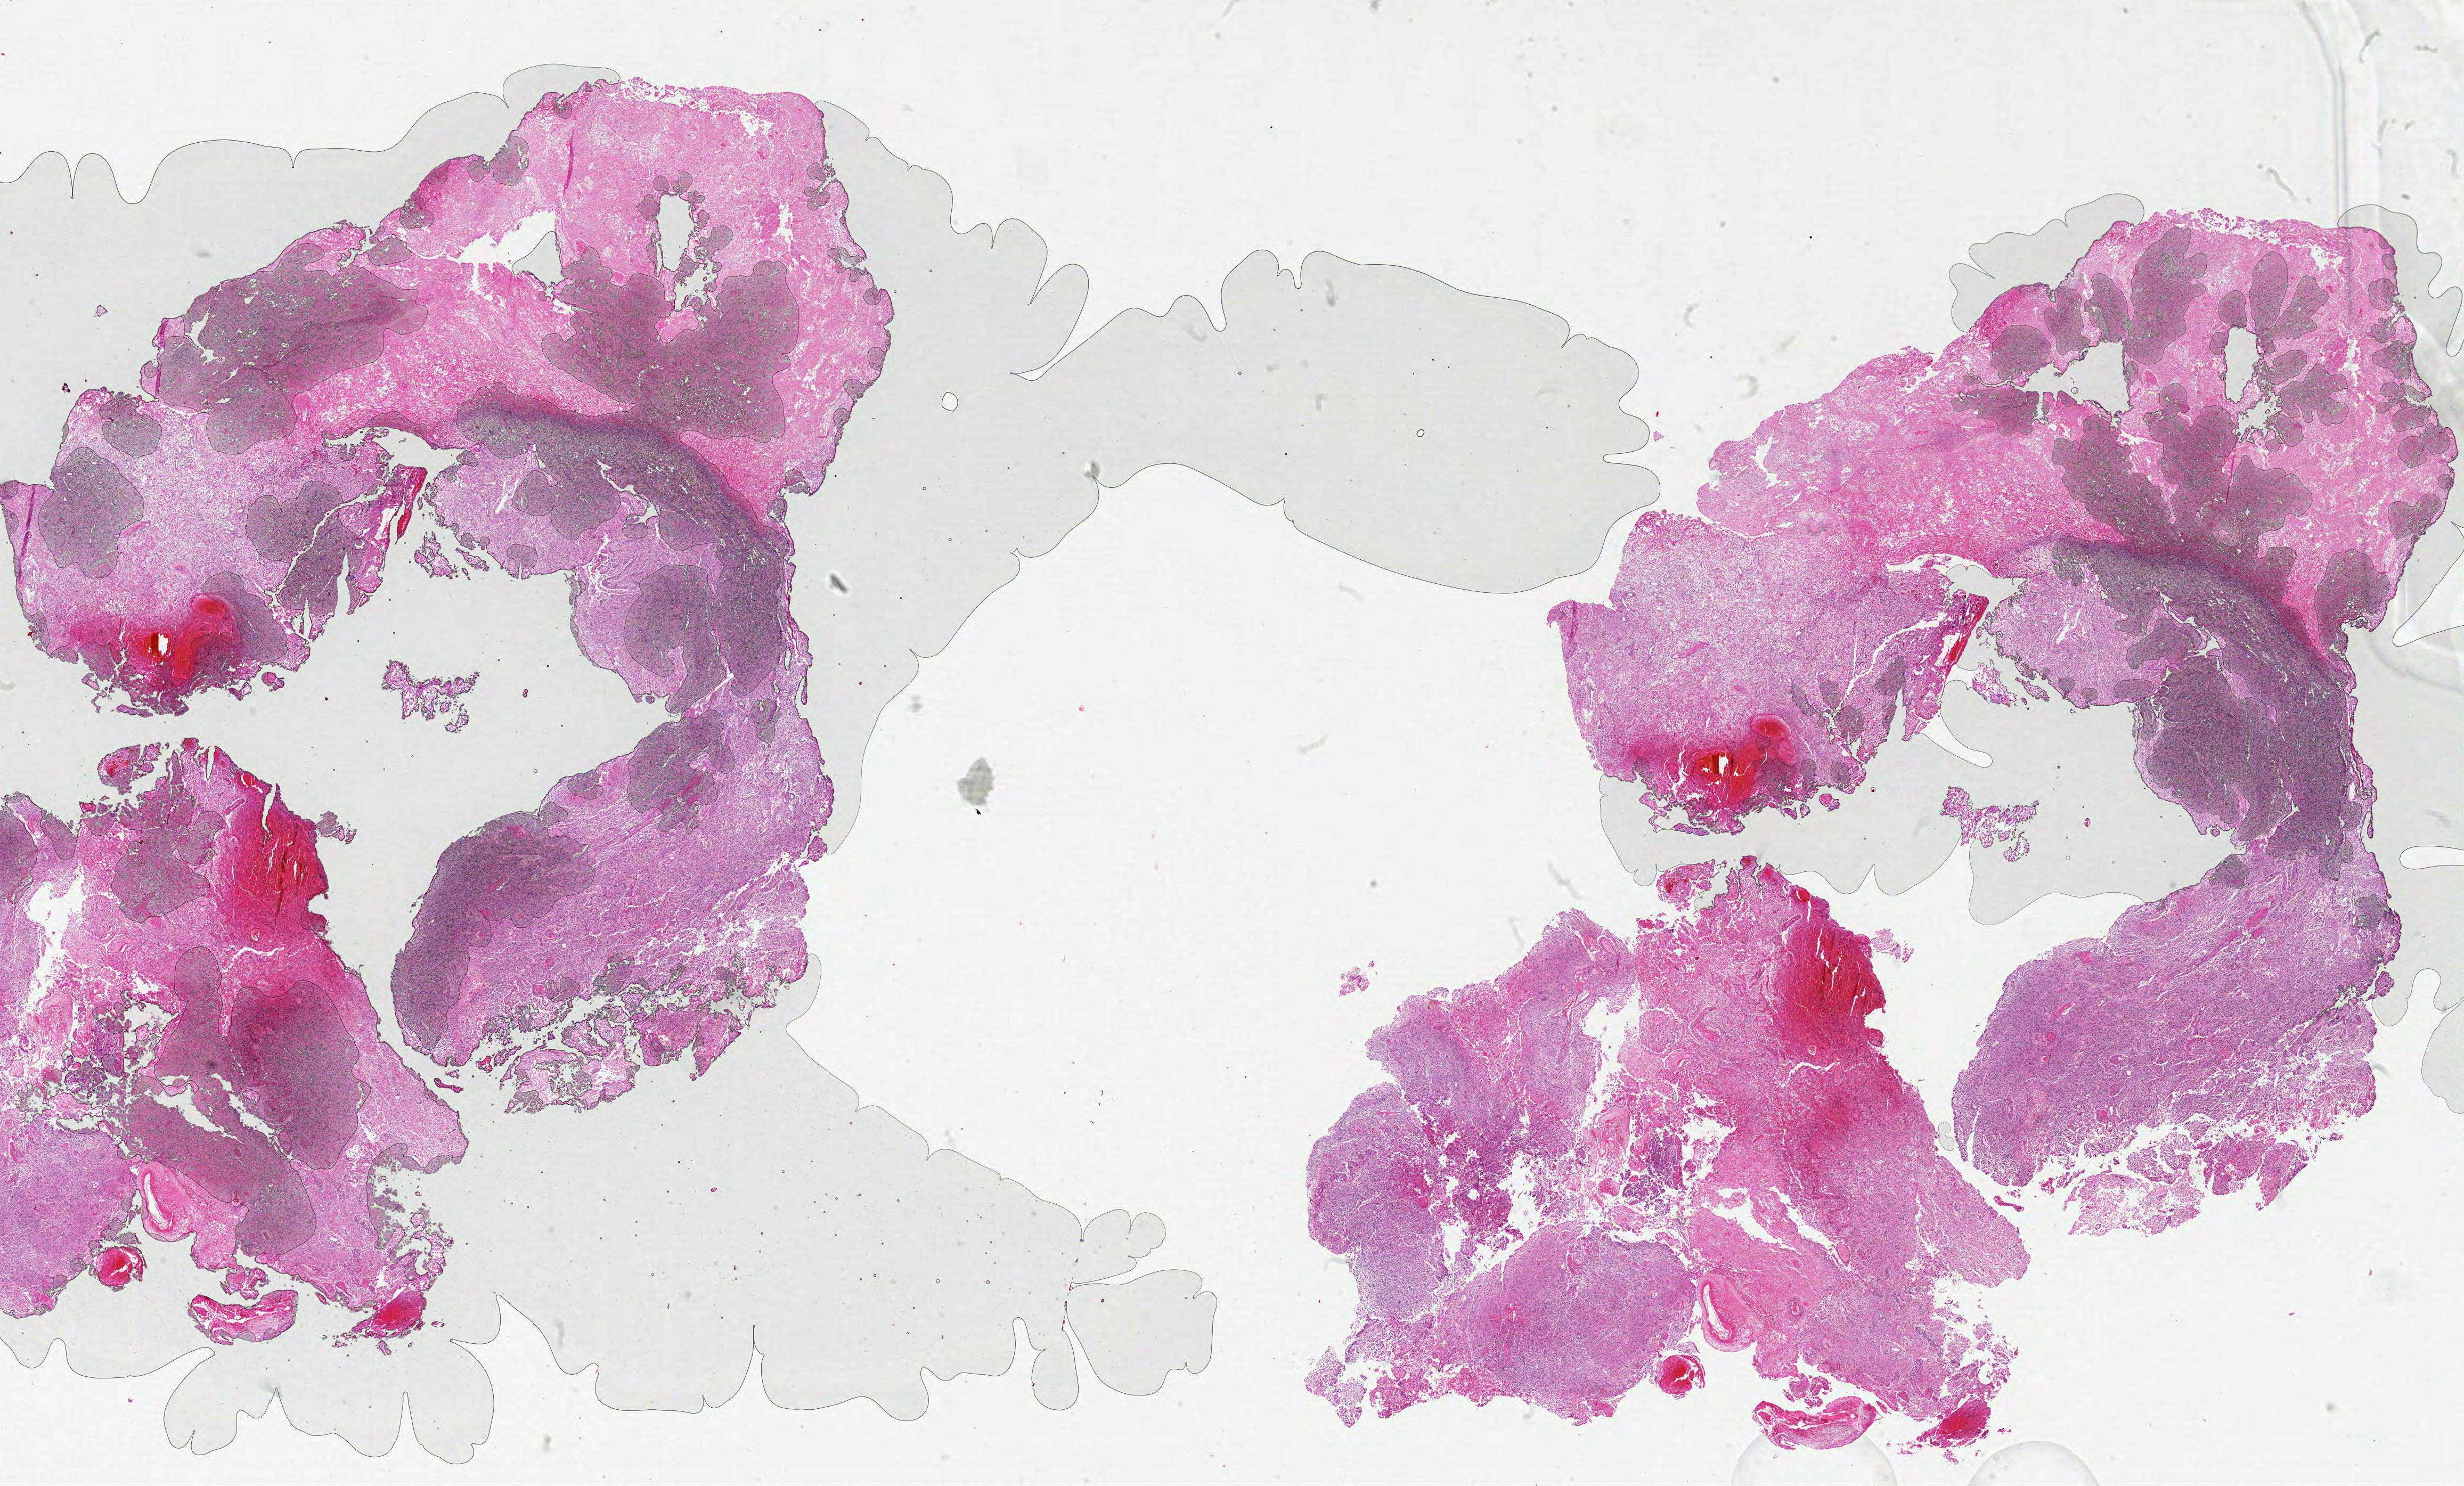
H&E whole-slide image, shown as a low-resolution overview of the whole scanned area (about 37.0 x 22.3 mm, acquisition: 20x scan), formalin-fixed paraffin-embedded (FFPE) diagnostic section, sample: primary tumour, brain. Male, age 53 years at initial diagnosis.
• diagnosis: Glioblastoma